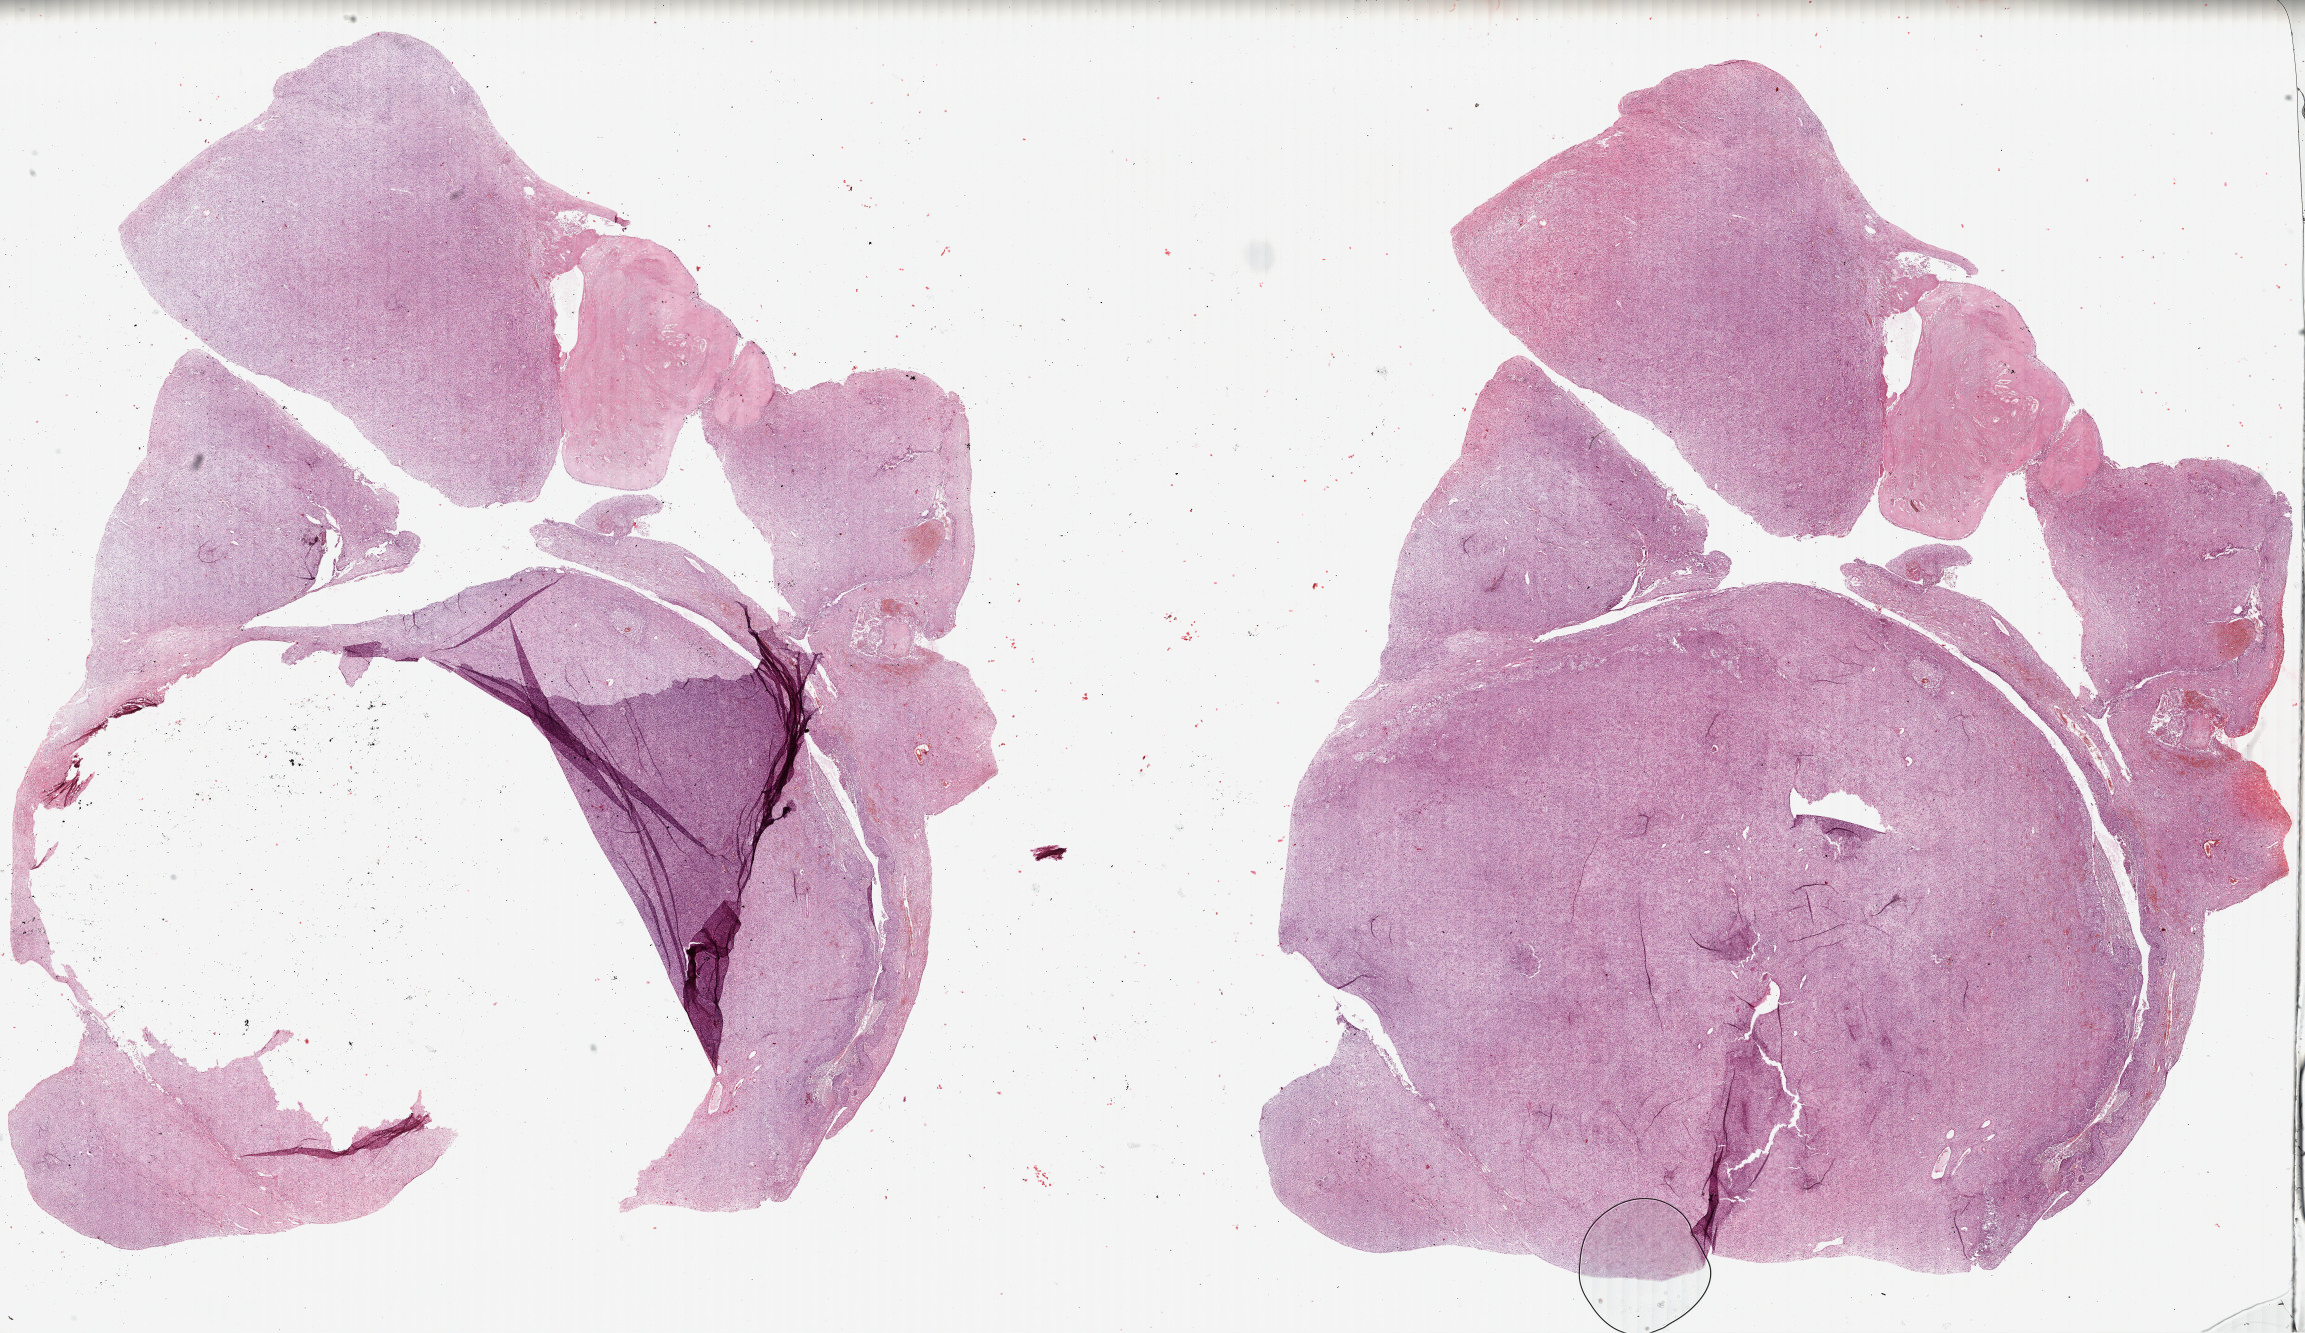
Whole-slide histology image, H&E-stained — low-resolution overview of the scanned area, about 36.2 x 21.0 mm (acquisition: 40x scan), FFPE section, sample: primary tumour, uterus. Female, age 55 years at initial diagnosis.
FIGO stage: IB. Pathologic diagnosis: Mullerian mixed tumor (endometrium).